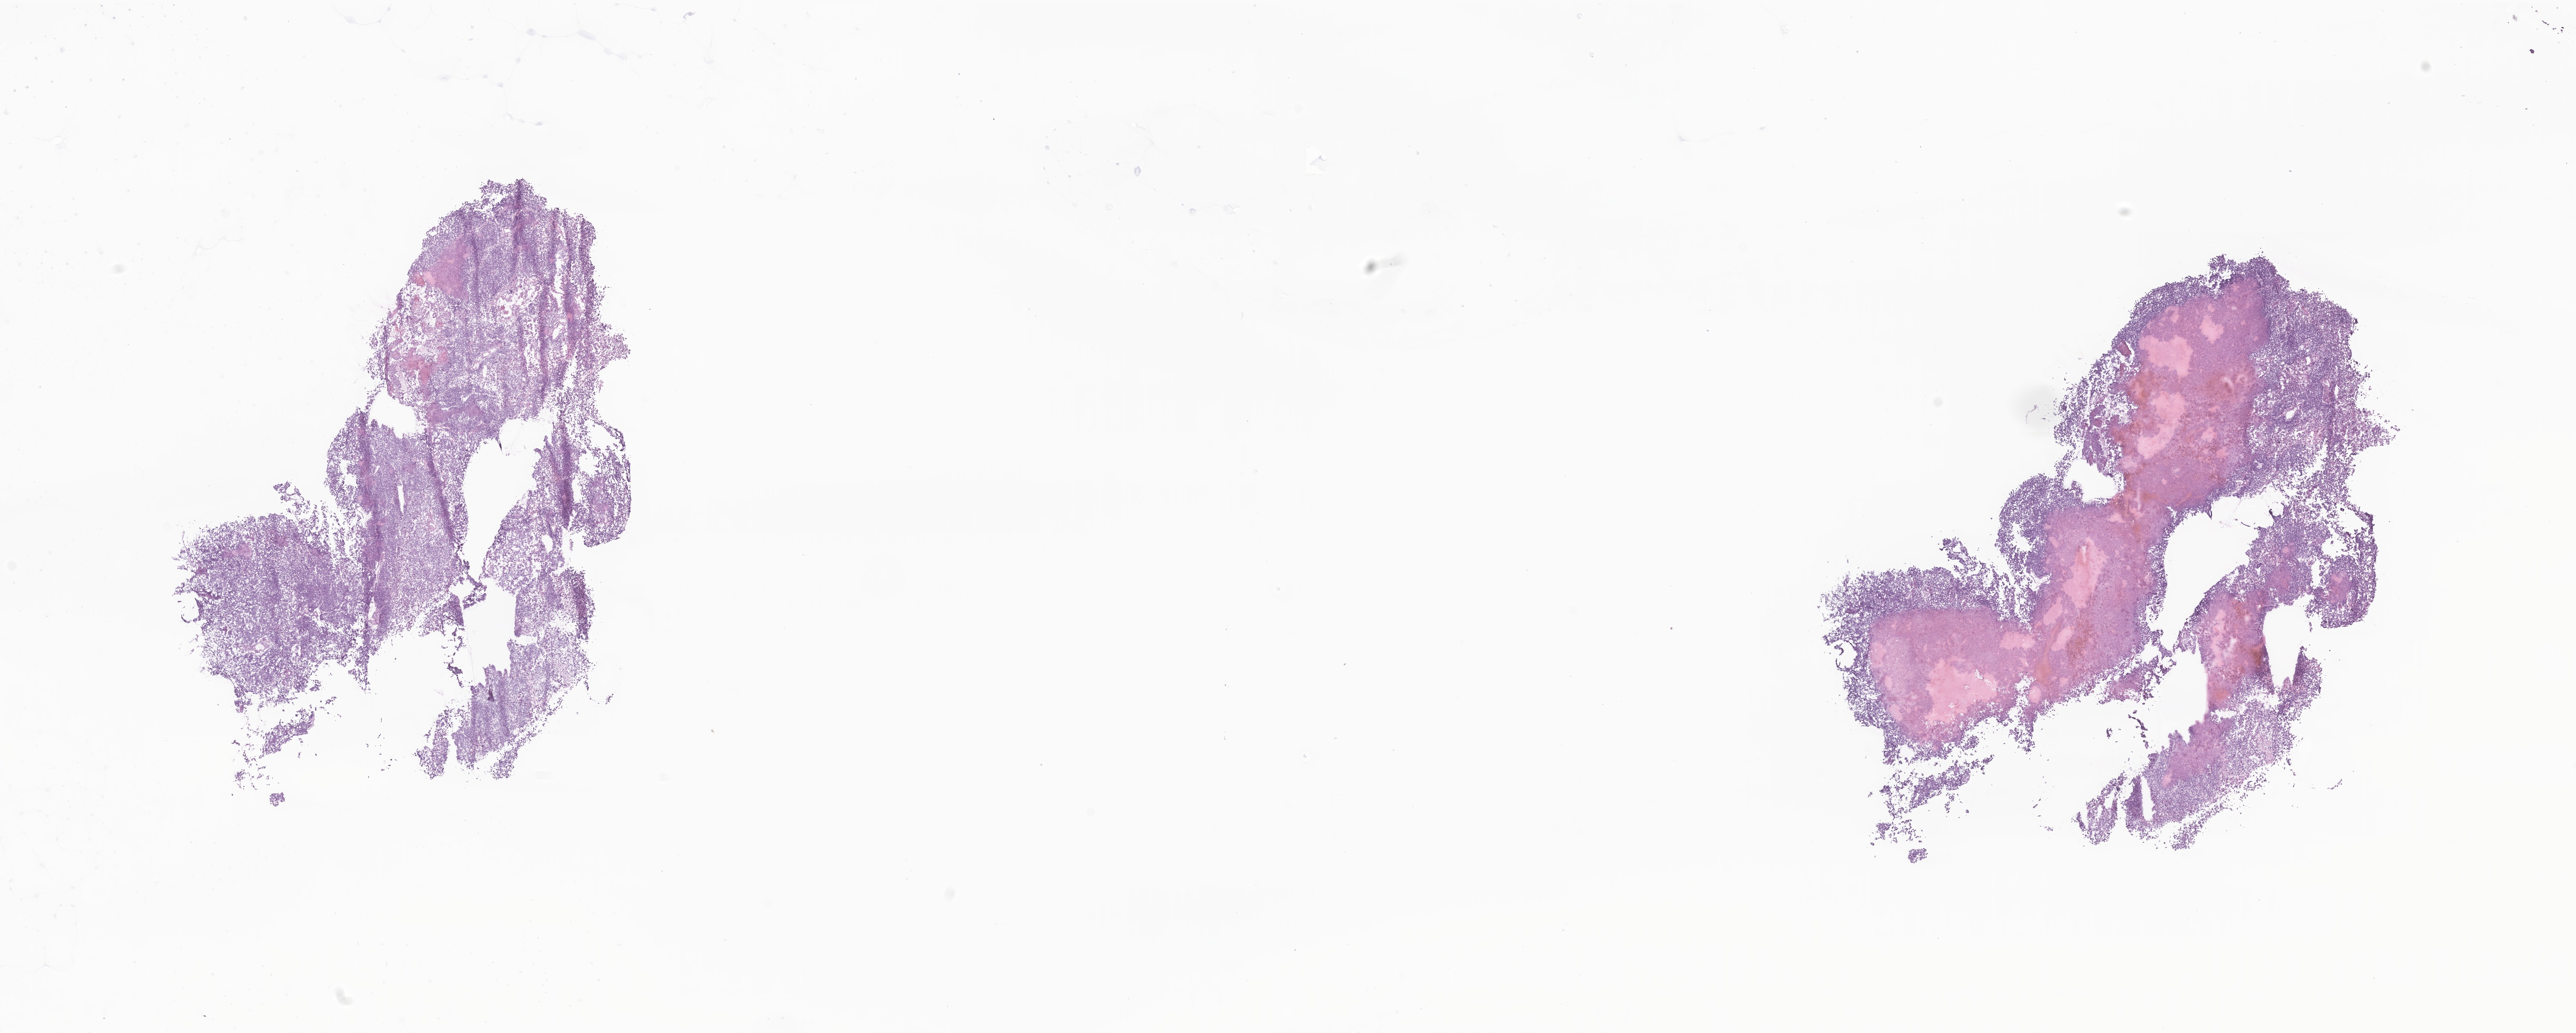
H&E whole-slide image of tumor tissue from the brain, a low-resolution overview of the entire scanned area, about 27.3 x 11.0 mm. Male patient, age 191 months (15 years 11 months).
Specimen: frozen section.